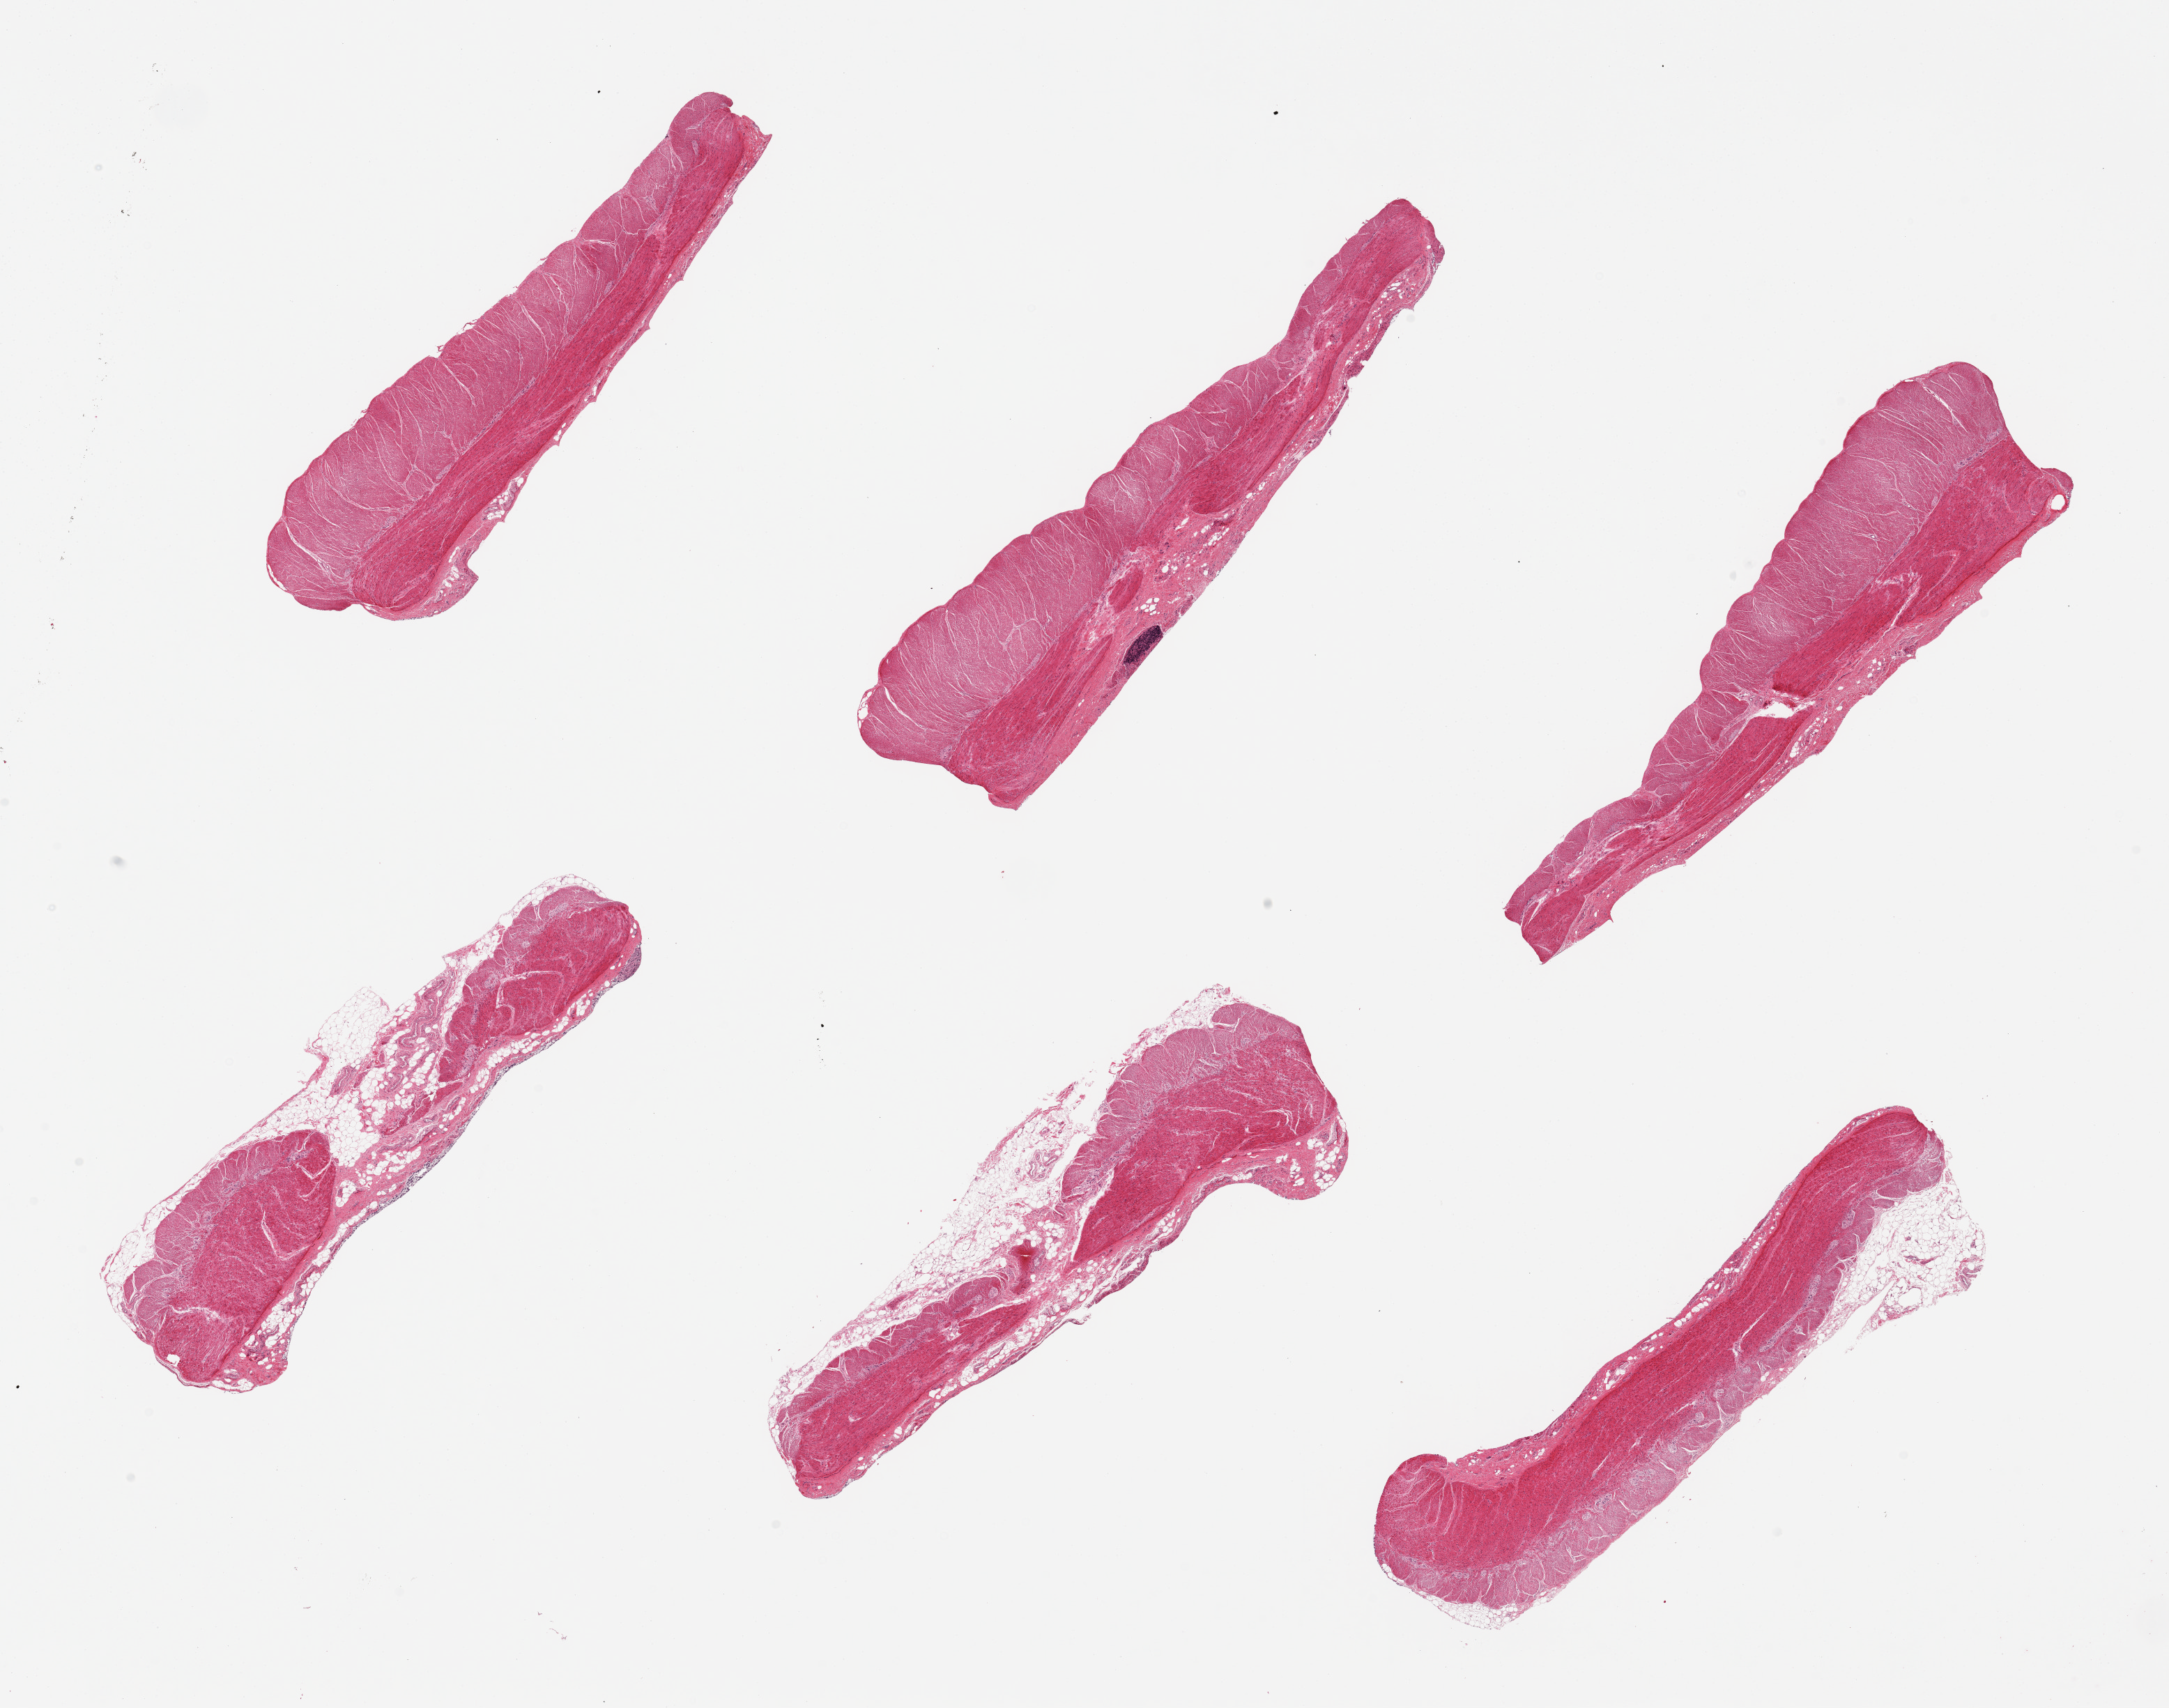
Hematoxylin and eosin (H&E) whole-slide image, shown as a low-resolution overview of the whole scanned area (about 24.6 x 19.4 mm), PAXgene-fixed paraffin-embedded (PFPE) section, section of sigmoid colon (target tissue), tissue donor sample. Male donor.
• review note (as recorded): 6 pieces, up to 8x2mm; Muscualris; a few nubbings of adherent fat, on 2